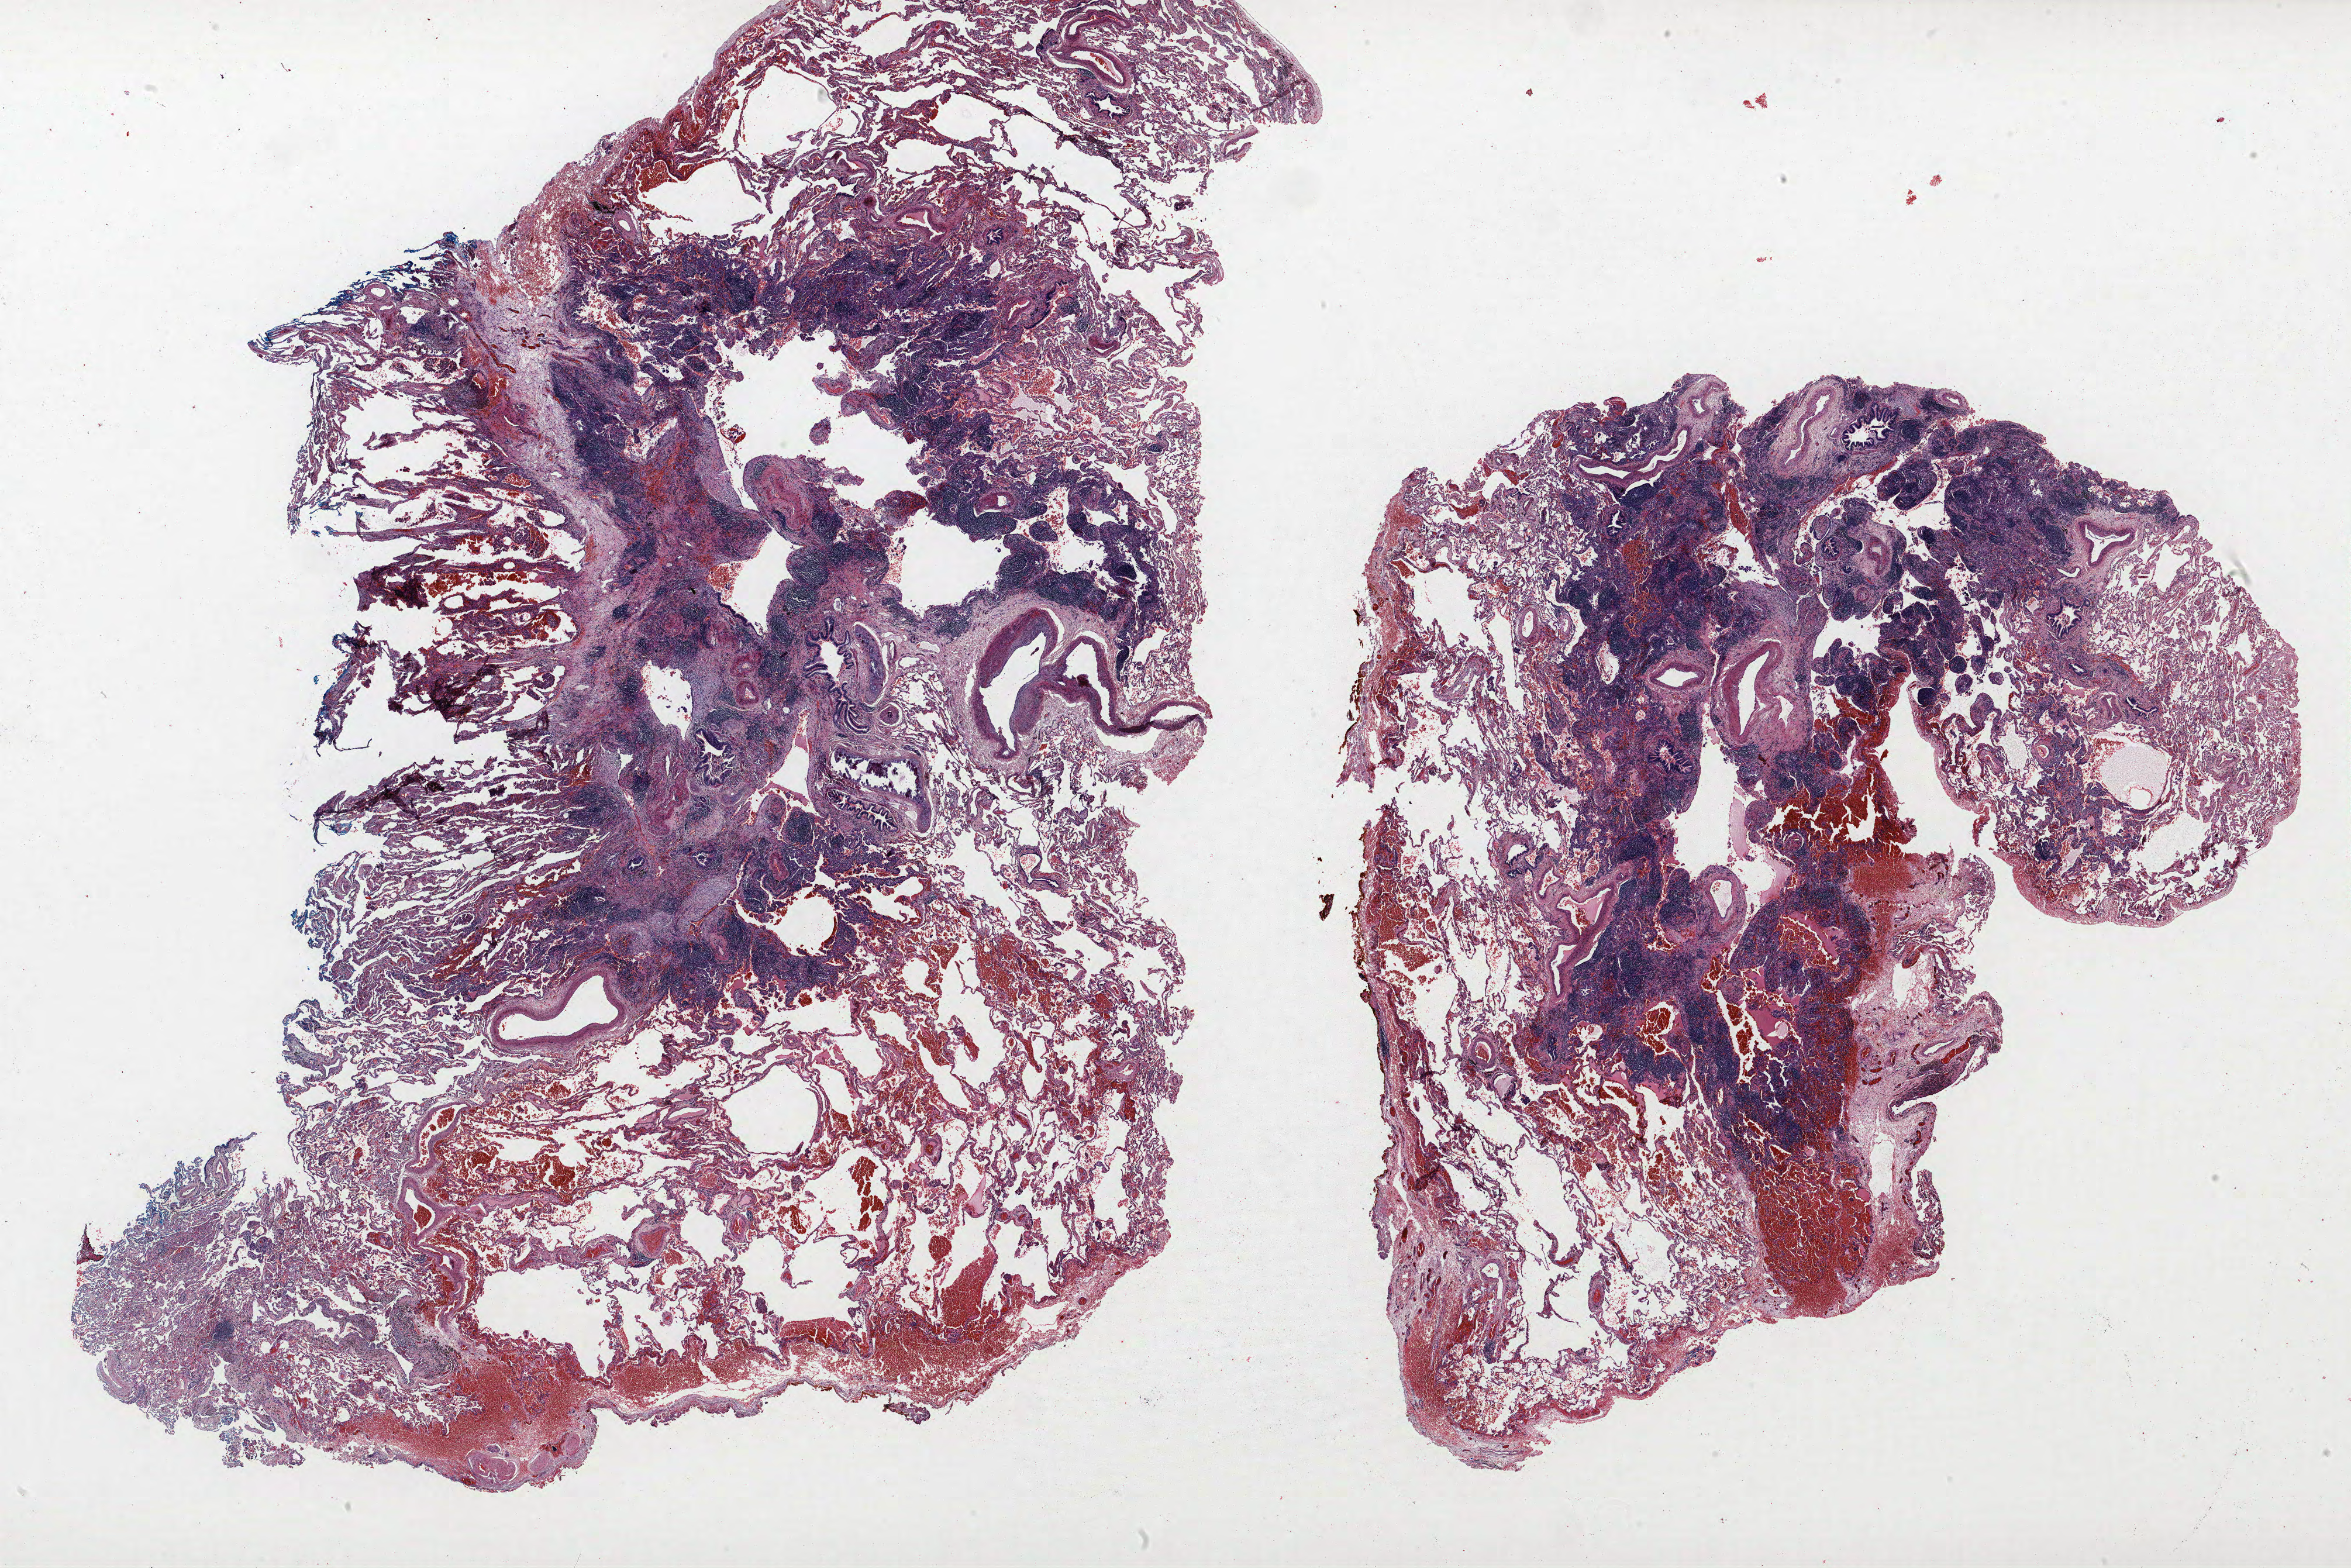
Whole-slide histology image, H&E-stained, whole scanned area (about 32.2 x 21.5 mm, slide scanned at 40x) shown as a low-resolution overview. FFPE section. Lung. Female patient, aged 59 at enrolment. Grade: moderately differentiated (G2).
* stage (AJCC 6th edition): IA
* tumour size (pathology): 11 mm
* primary tumour location (clinical record): right middle lobe
* participant's lung-cancer diagnosis: Adenocarcinoma, NOS
* note: participant had 2 primary lung cancers recorded; fields above describe the first